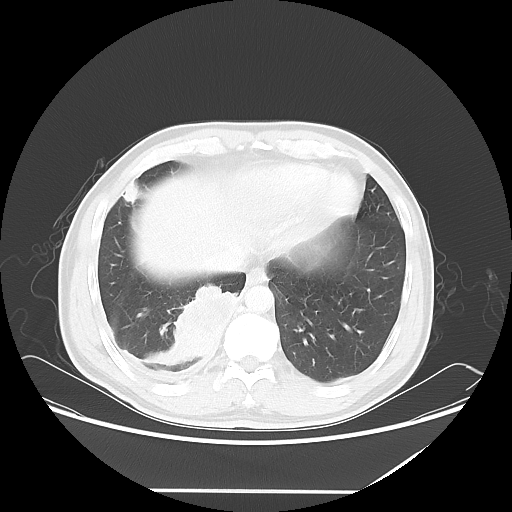
Chest CT, one axial slice; slice 17 of 60 in the series (ordered by position); lung window (W 1500 / L -600 HU); 5 mm slice thickness; 512 × 512 image matrix, field of view 419 × 419 mm. Patient: male, 48 years. Case-level facts recorded for this patient, not image findings: clinical TNM (as recorded): T3 N3 M1a.
Annotated regions visible in this slice (bounding box drawn by a radiologist):
- lung tumour (recorded histology: squamous cell carcinoma): bounding box [x1, y1, x2, y2] px = [166, 280, 236, 361]